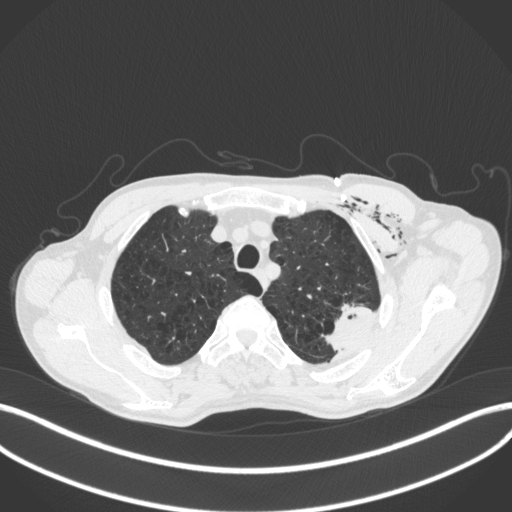
Chest CT, one axial slice; reconstruction kernel B31f; 120 kVp; lung window (W 1500 / L -600 HU); 1 mm slice thickness; 512 × 512 image matrix, field of view 400 × 400 mm. Patient: male, 58 years. From the clinical record (not read from this slice): clinical TNM (as recorded): T3 N0 M0.
Annotated regions visible in this slice (rectangle marked by the reading radiologist):
- lung tumour (recorded histology: adenocarcinoma): bounding box <323,301,380,360> (left, top, right, bottom; pixels)